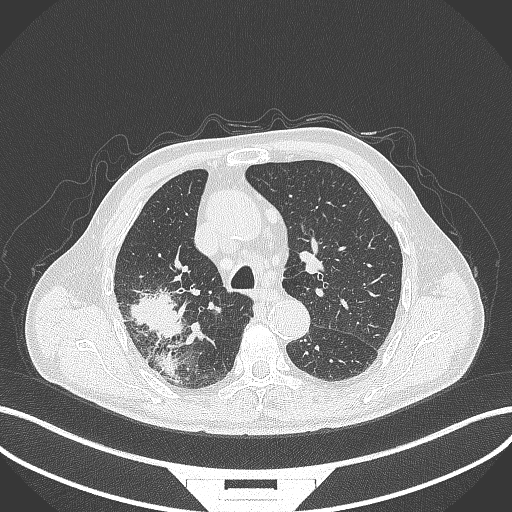
Chest CT, one axial slice. Position 284 of 429 along the scan axis. Reconstruction kernel B70f. Lung window (W 1500 / L -600 HU). 1 mm slice thickness. 512 × 512 image matrix, field of view 400 × 400 mm. Patient: male, 72 years. Case-level facts recorded for this patient, not image findings: clinical TNM (as recorded): T3 N2 M0.
Outlined on this slice (rectangle marked by the reading radiologist):
- lung tumour (recorded histology: adenocarcinoma): bounding box <128,291,188,340> (left, top, right, bottom; pixels)